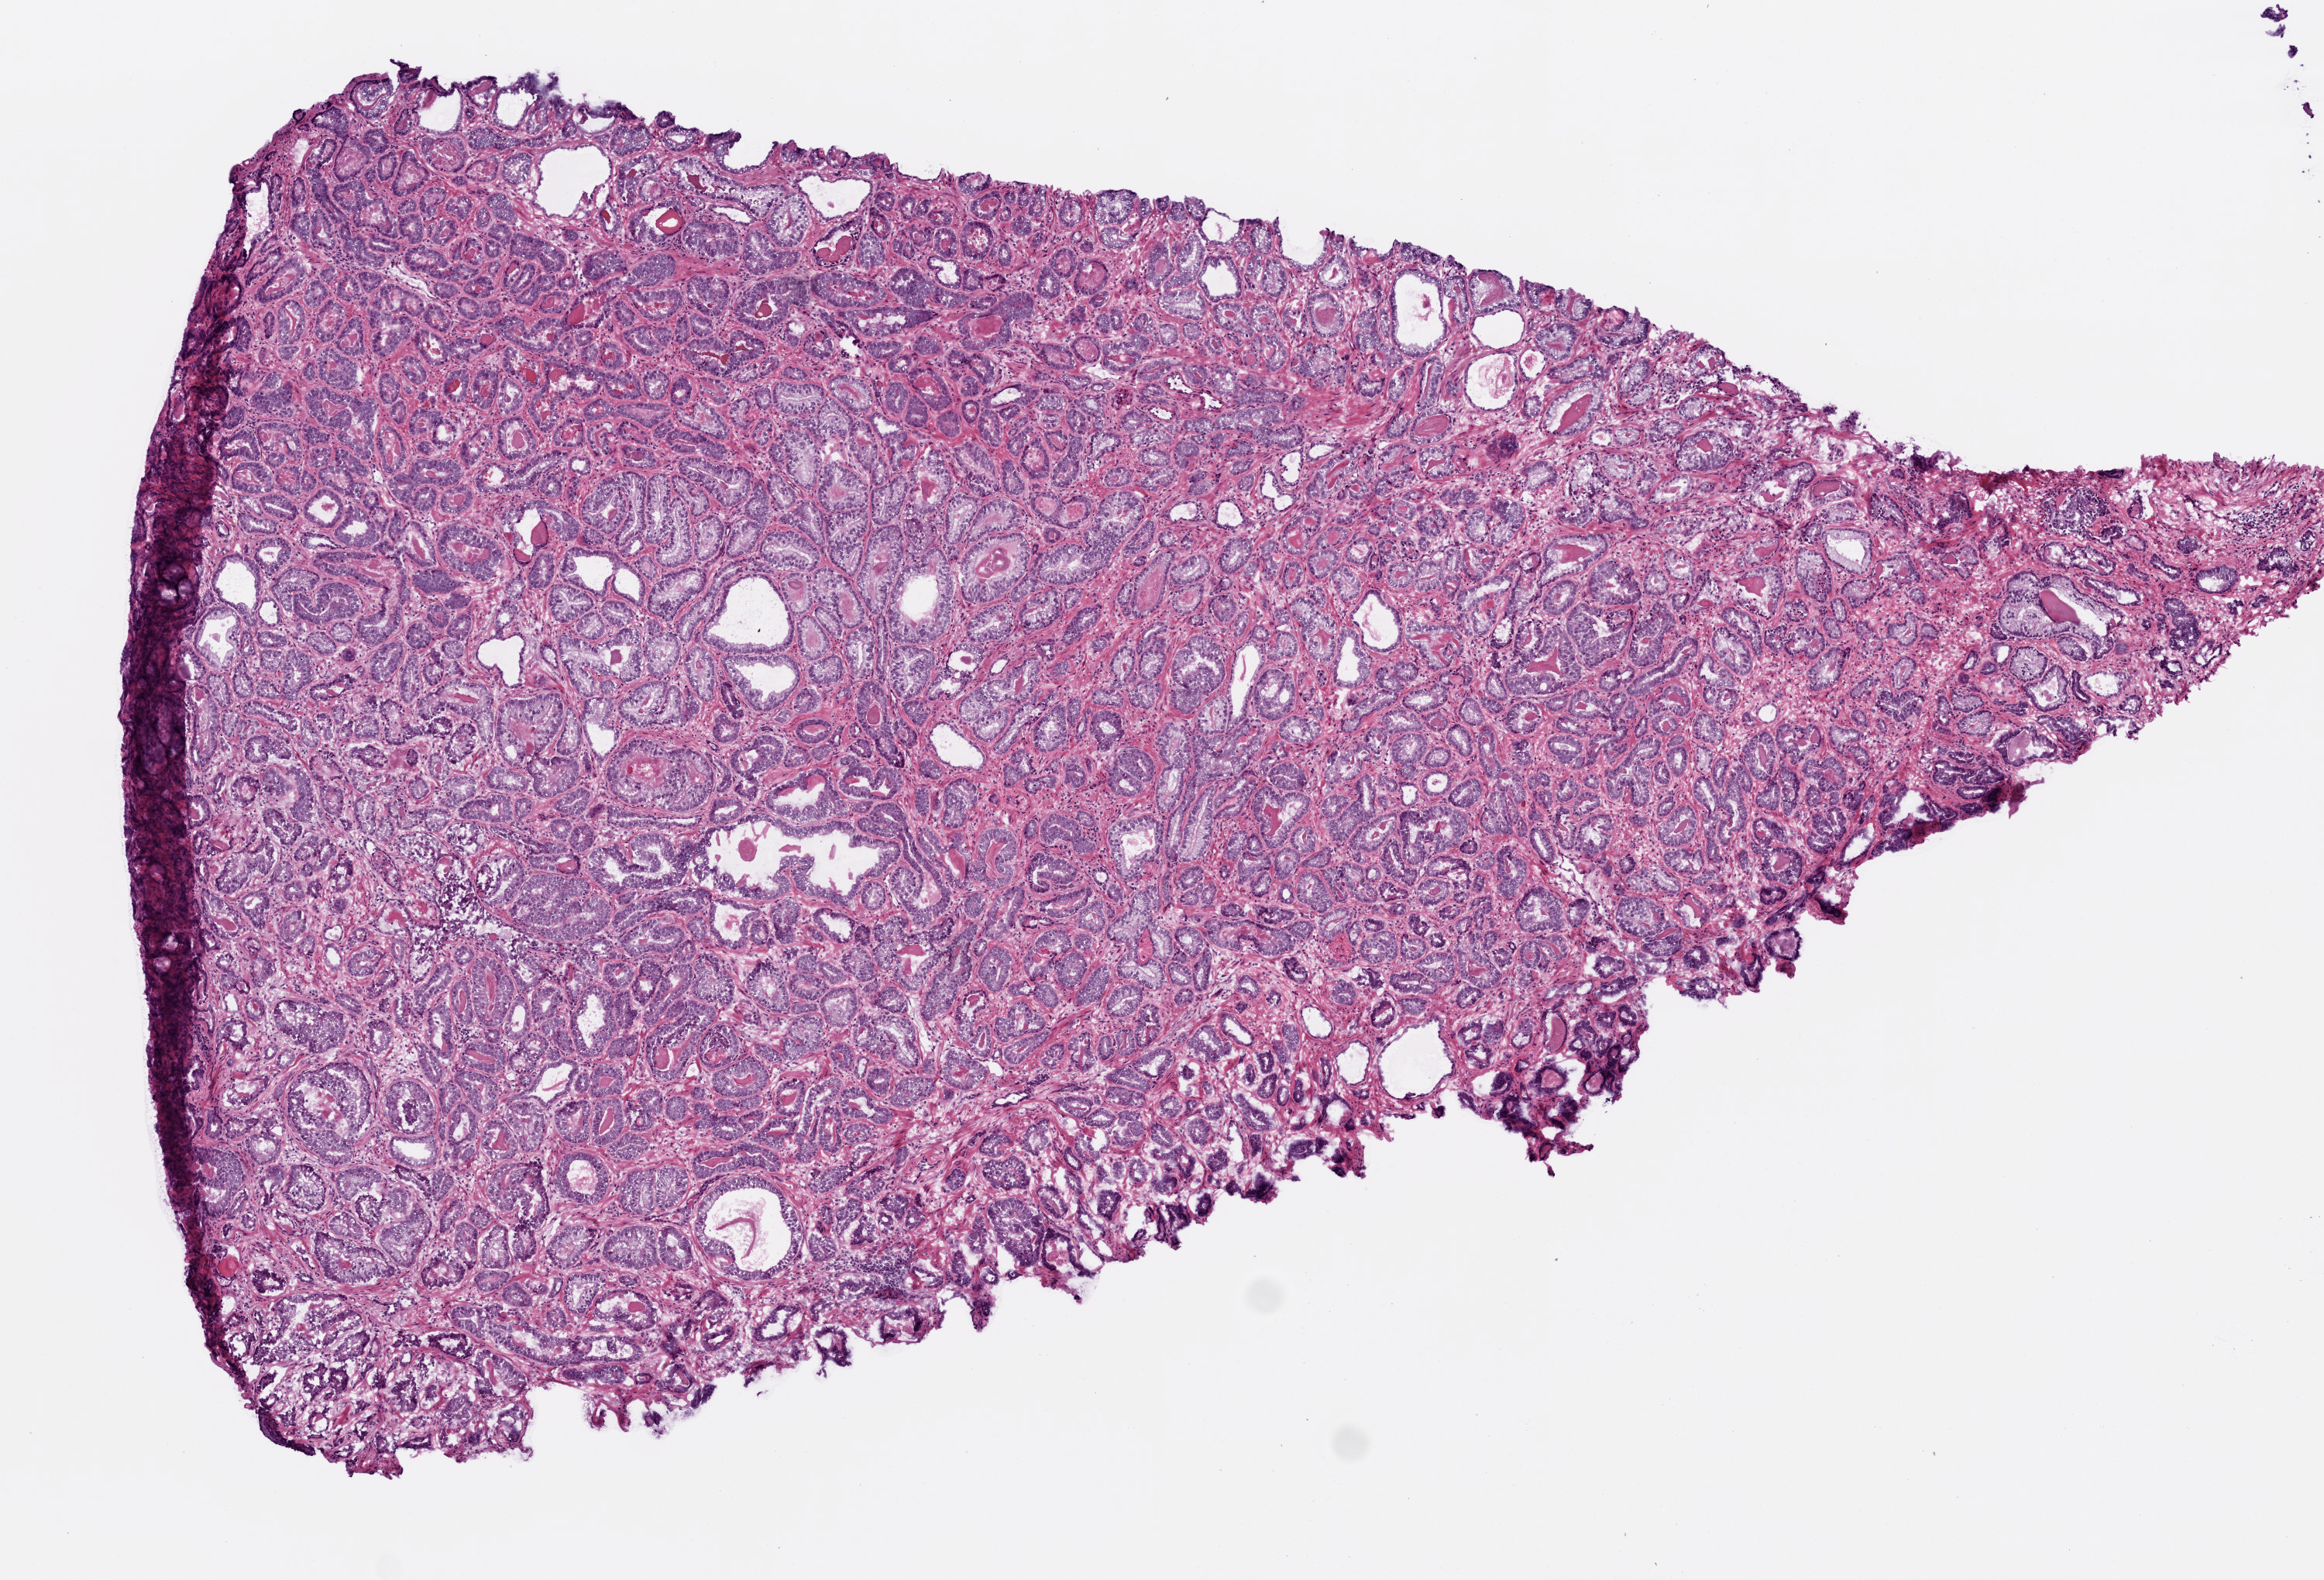
Digitized H&E-stained tissue section (whole slide) — shown as a low-resolution overview of the whole scanned area (about 6.0 x 4.1 mm, from a 20x scan). Frozen section from the top of the tissue portion. Prostate, primary tumour sample. Male patient; age at initial diagnosis 64 years.
Pathologic diagnosis: Acinar cell carcinoma (prostate gland).